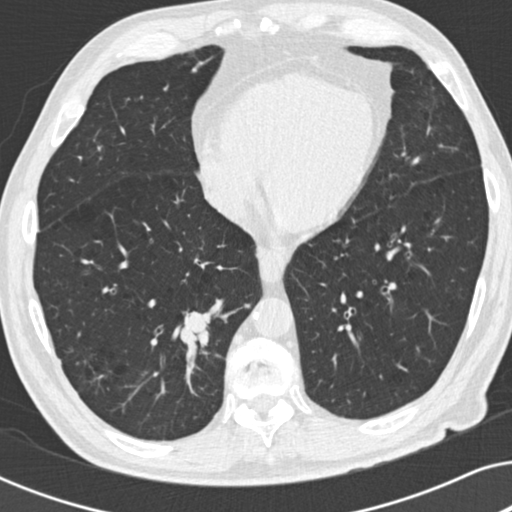
Low-dose screening chest CT, one axial slice; position 81 of 191 along the scan axis; reconstruction kernel B30f; lung window (W 1500 / L -600 HU); 2 mm slice thickness; 512 × 512 image matrix.
Annotated regions visible in this slice (outlined manually by an expert reader):
- lesion 1 (tumor, lower lobe of right lung): box from (x=176, y=309) to (x=210, y=347) px